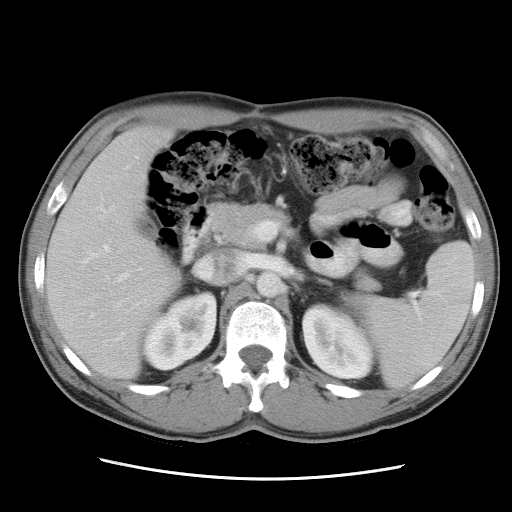
Contrast-enhanced abdominal CT, one axial slice. Position 16 of 34 along the scan axis. Reconstruction kernel STANDARD. 120 kVp. Intravenous contrast given. Soft-tissue window (W 400 / L 40 HU). 7.5 mm slice thickness. 512 × 512 image matrix, field of view 360 × 360 mm. Male patient, age 40 years. Case-level facts recorded for this patient, not image findings: diagnosis: colorectal cancer liver metastases, imaged before liver resection; multiple liver metastases: yes; largest metastasis: 1.5 cm; disease in both lobes: yes.
Annotated regions visible in this slice (manually delineated by an expert):
- liver: bounding box <47,128,183,378> (left, top, right, bottom; pixels)
- planned liver remnant (the part of the liver to remain after resection): <47,128,183,378>
- portal vein (with intrahepatic branches): <104,228,257,283>